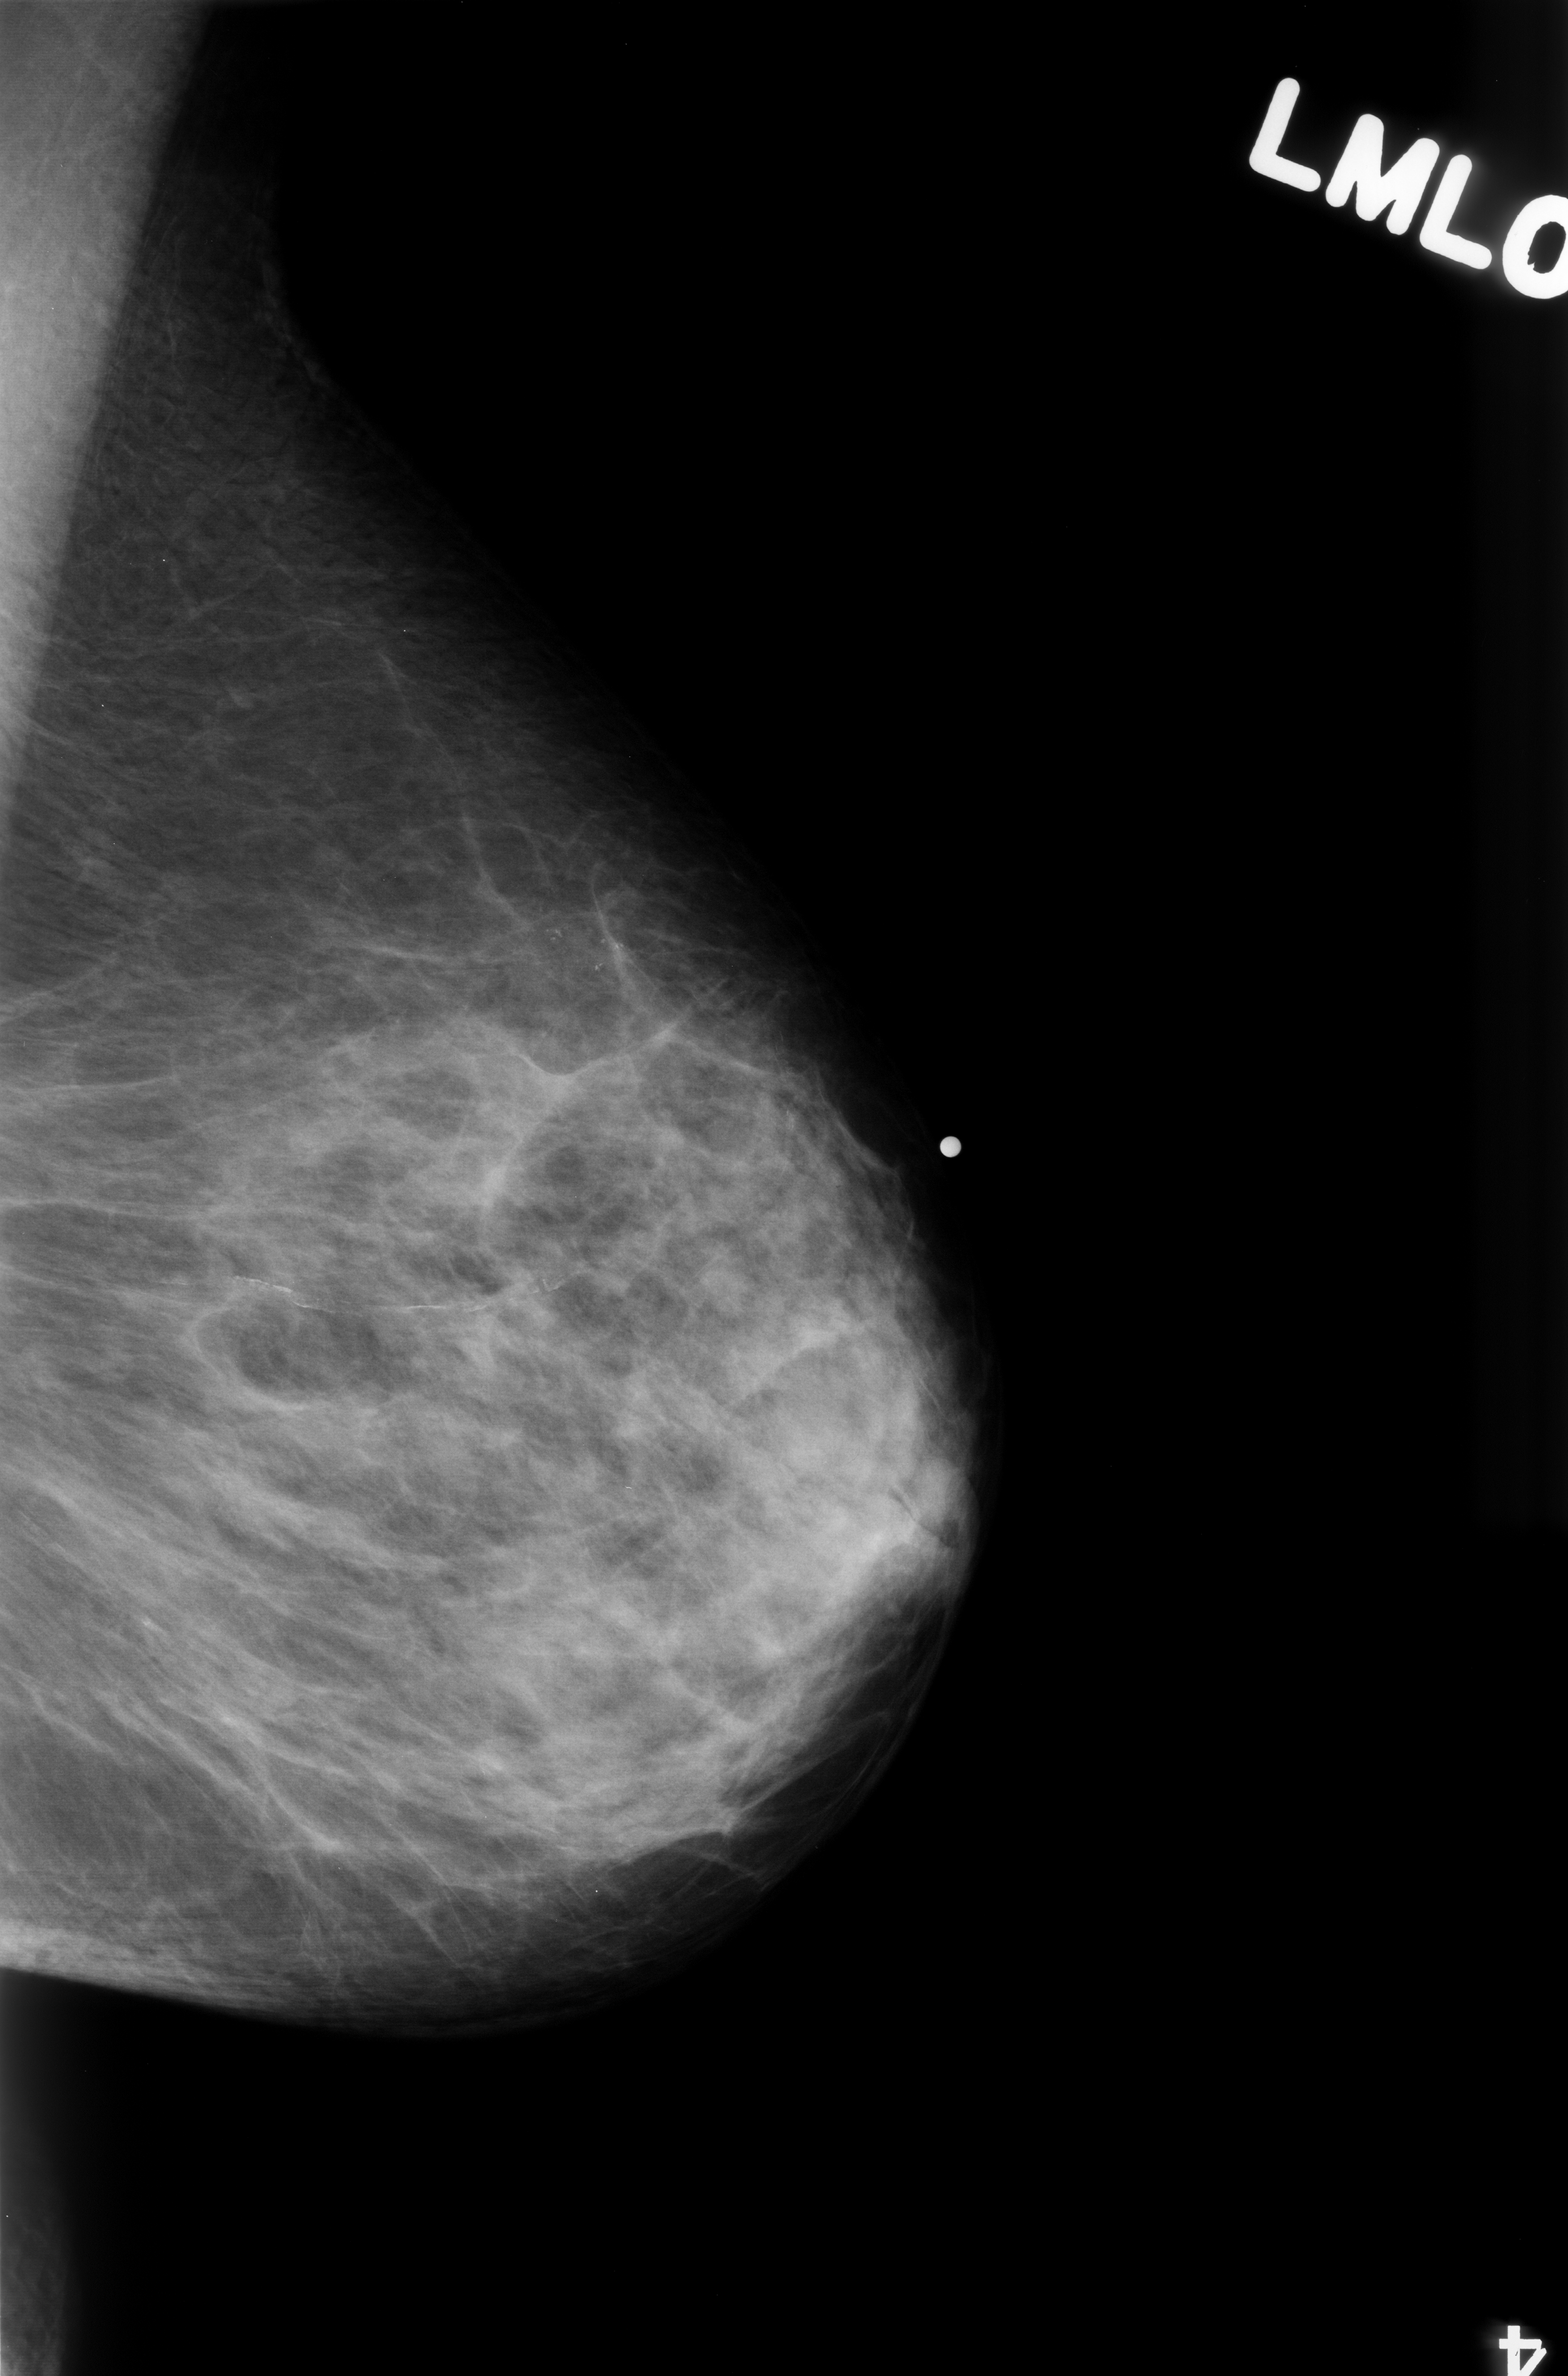
Digitized screen-film mammogram; left breast; MLO view; BI-RADS breast density category 2 (scale 1–4).
Marked abnormality: calcifications, morphology pleomorphic, distribution clustered; BI-RADS assessment category 4; pathology result (as recorded, not read from the image): benign.